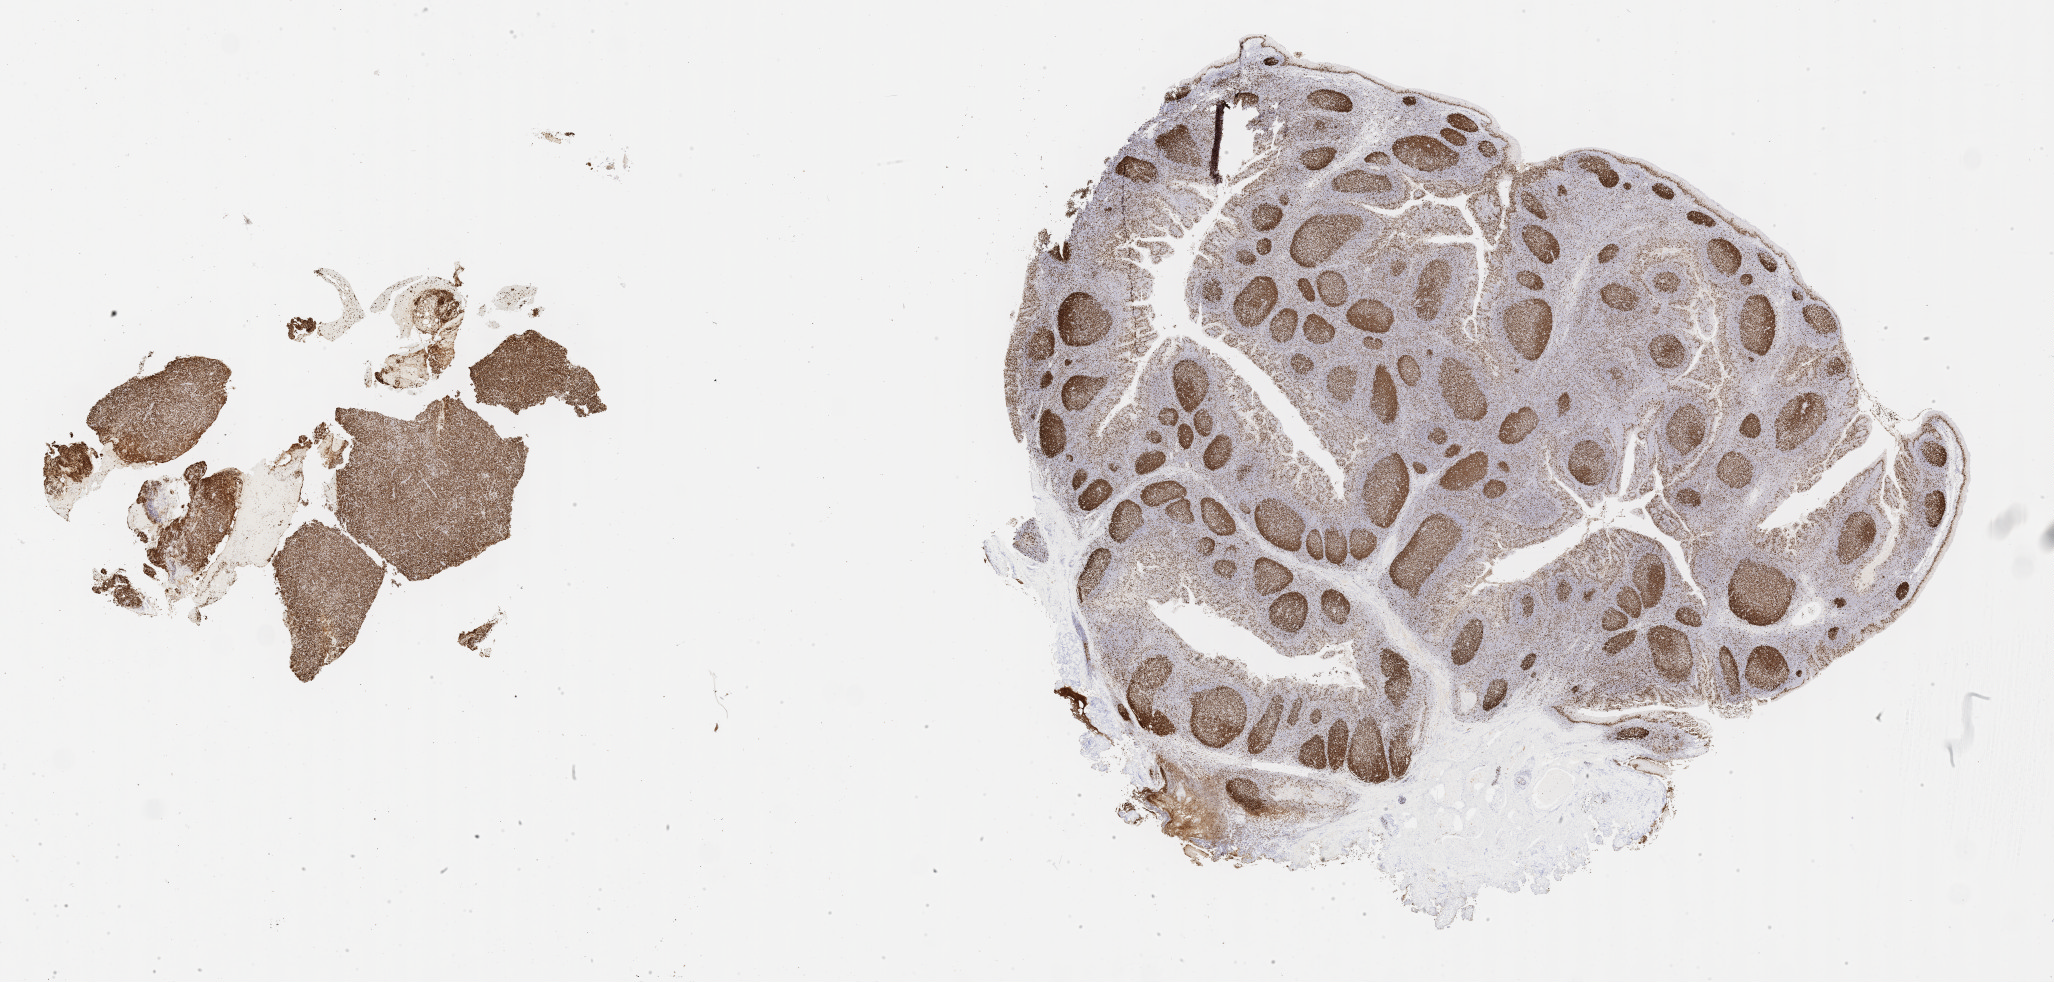
Immunohistochemistry (IHC) whole-slide image stained for Ki-67, shown as a low-resolution overview of the whole scanned area (about 33.2 x 15.9 mm), specimen: tumor tissue, anatomic site: lymph node. Patient female; aged 71.
Diagnosis: Diffuse large B-cell lymphoma, NOS.